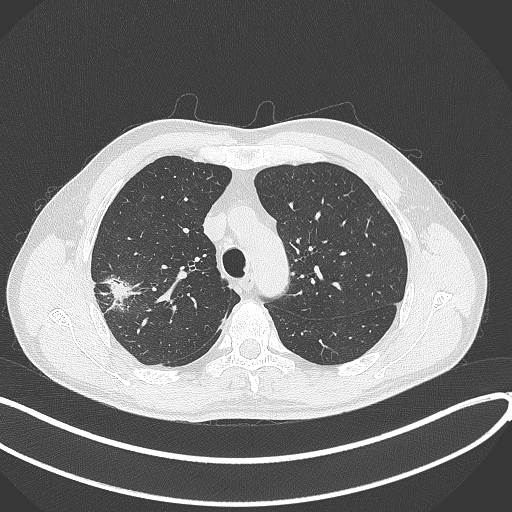
Chest CT, one axial slice; position 312 of 381 along the scan axis; reconstruction kernel B70f; 120 kVp; lung window (W 1500 / L -600 HU); 1 mm slice thickness; 512 × 512 image matrix, field of view 400 × 400 mm. Patient: male, 62 years. Case-level facts recorded for this patient, not image findings: clinical TNM (as recorded): T1c N0 M0.
Annotated regions visible in this slice (bounding box drawn by a radiologist):
- lung tumour (recorded histology: adenocarcinoma): box from (x=101, y=274) to (x=144, y=308) px